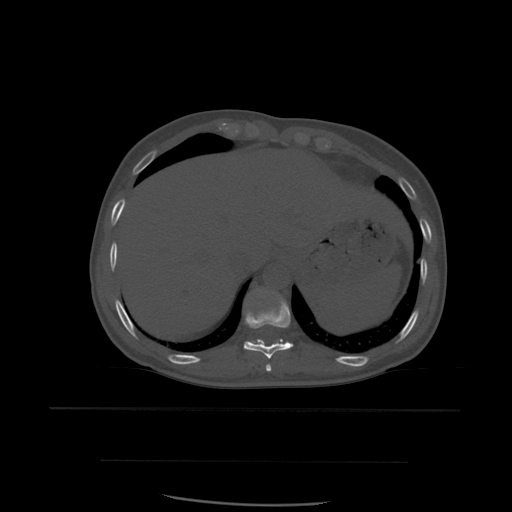
CT including the spine, one axial slice; position 312 of 574 along the scan axis; bone window (W 1800 / L 400 HU); 512 × 512 image matrix, field of view 392 × 392 mm. Patient age 48 years. Case-level facts recorded for this patient, not image findings: primary cancer: lung.
Structures marked on this image (semi-automatic segmentation, software-assisted and operator-edited):
- T10 vertebra: bounding box <244,295,293,359> (left, top, right, bottom; pixels)
- T11 vertebra: <249,294,289,346>
- T9 vertebra: <266,364,272,372>